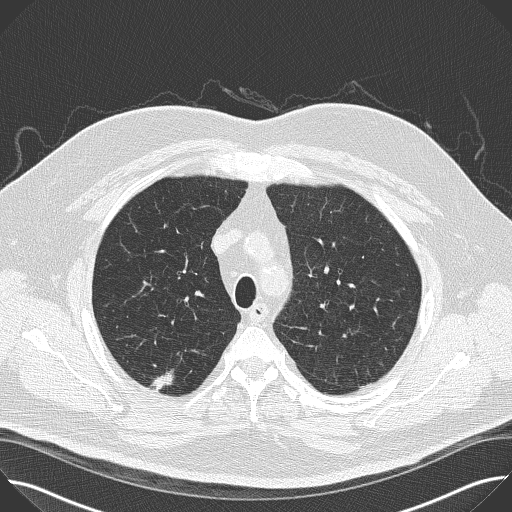
Low-dose screening chest CT, axial slice; first (baseline) screen; lung window (W 1500 / L -600 HU); 2 mm slice thickness; lung (sharp) reconstruction kernel (B50f); slice 124 of 160 in the series. Male, age 65 years at enrolment. Former smoker at enrolment.
- Expert-annotated lung lesion, box from (x=139, y=364) to (x=189, y=404) px.
- The screening reader recorded 2 non-calcified nodules or masses ≥4 mm on this exam; which of them this box marks is not recorded.
- Official screen result: positive, change unspecified: nodule(s) >= 4 mm or enlarging nodule(s), mass(es), or other non-specific abnormalities suspicious for lung cancer.
- Participant outcome: lung cancer diagnosed 47 days after this screen — bronchiolo-alveolar adenocarcinoma, NOS, right upper lobe, moderately differentiated (G2), stage IIA (AJCC 6th edition), 14 mm at pathology.